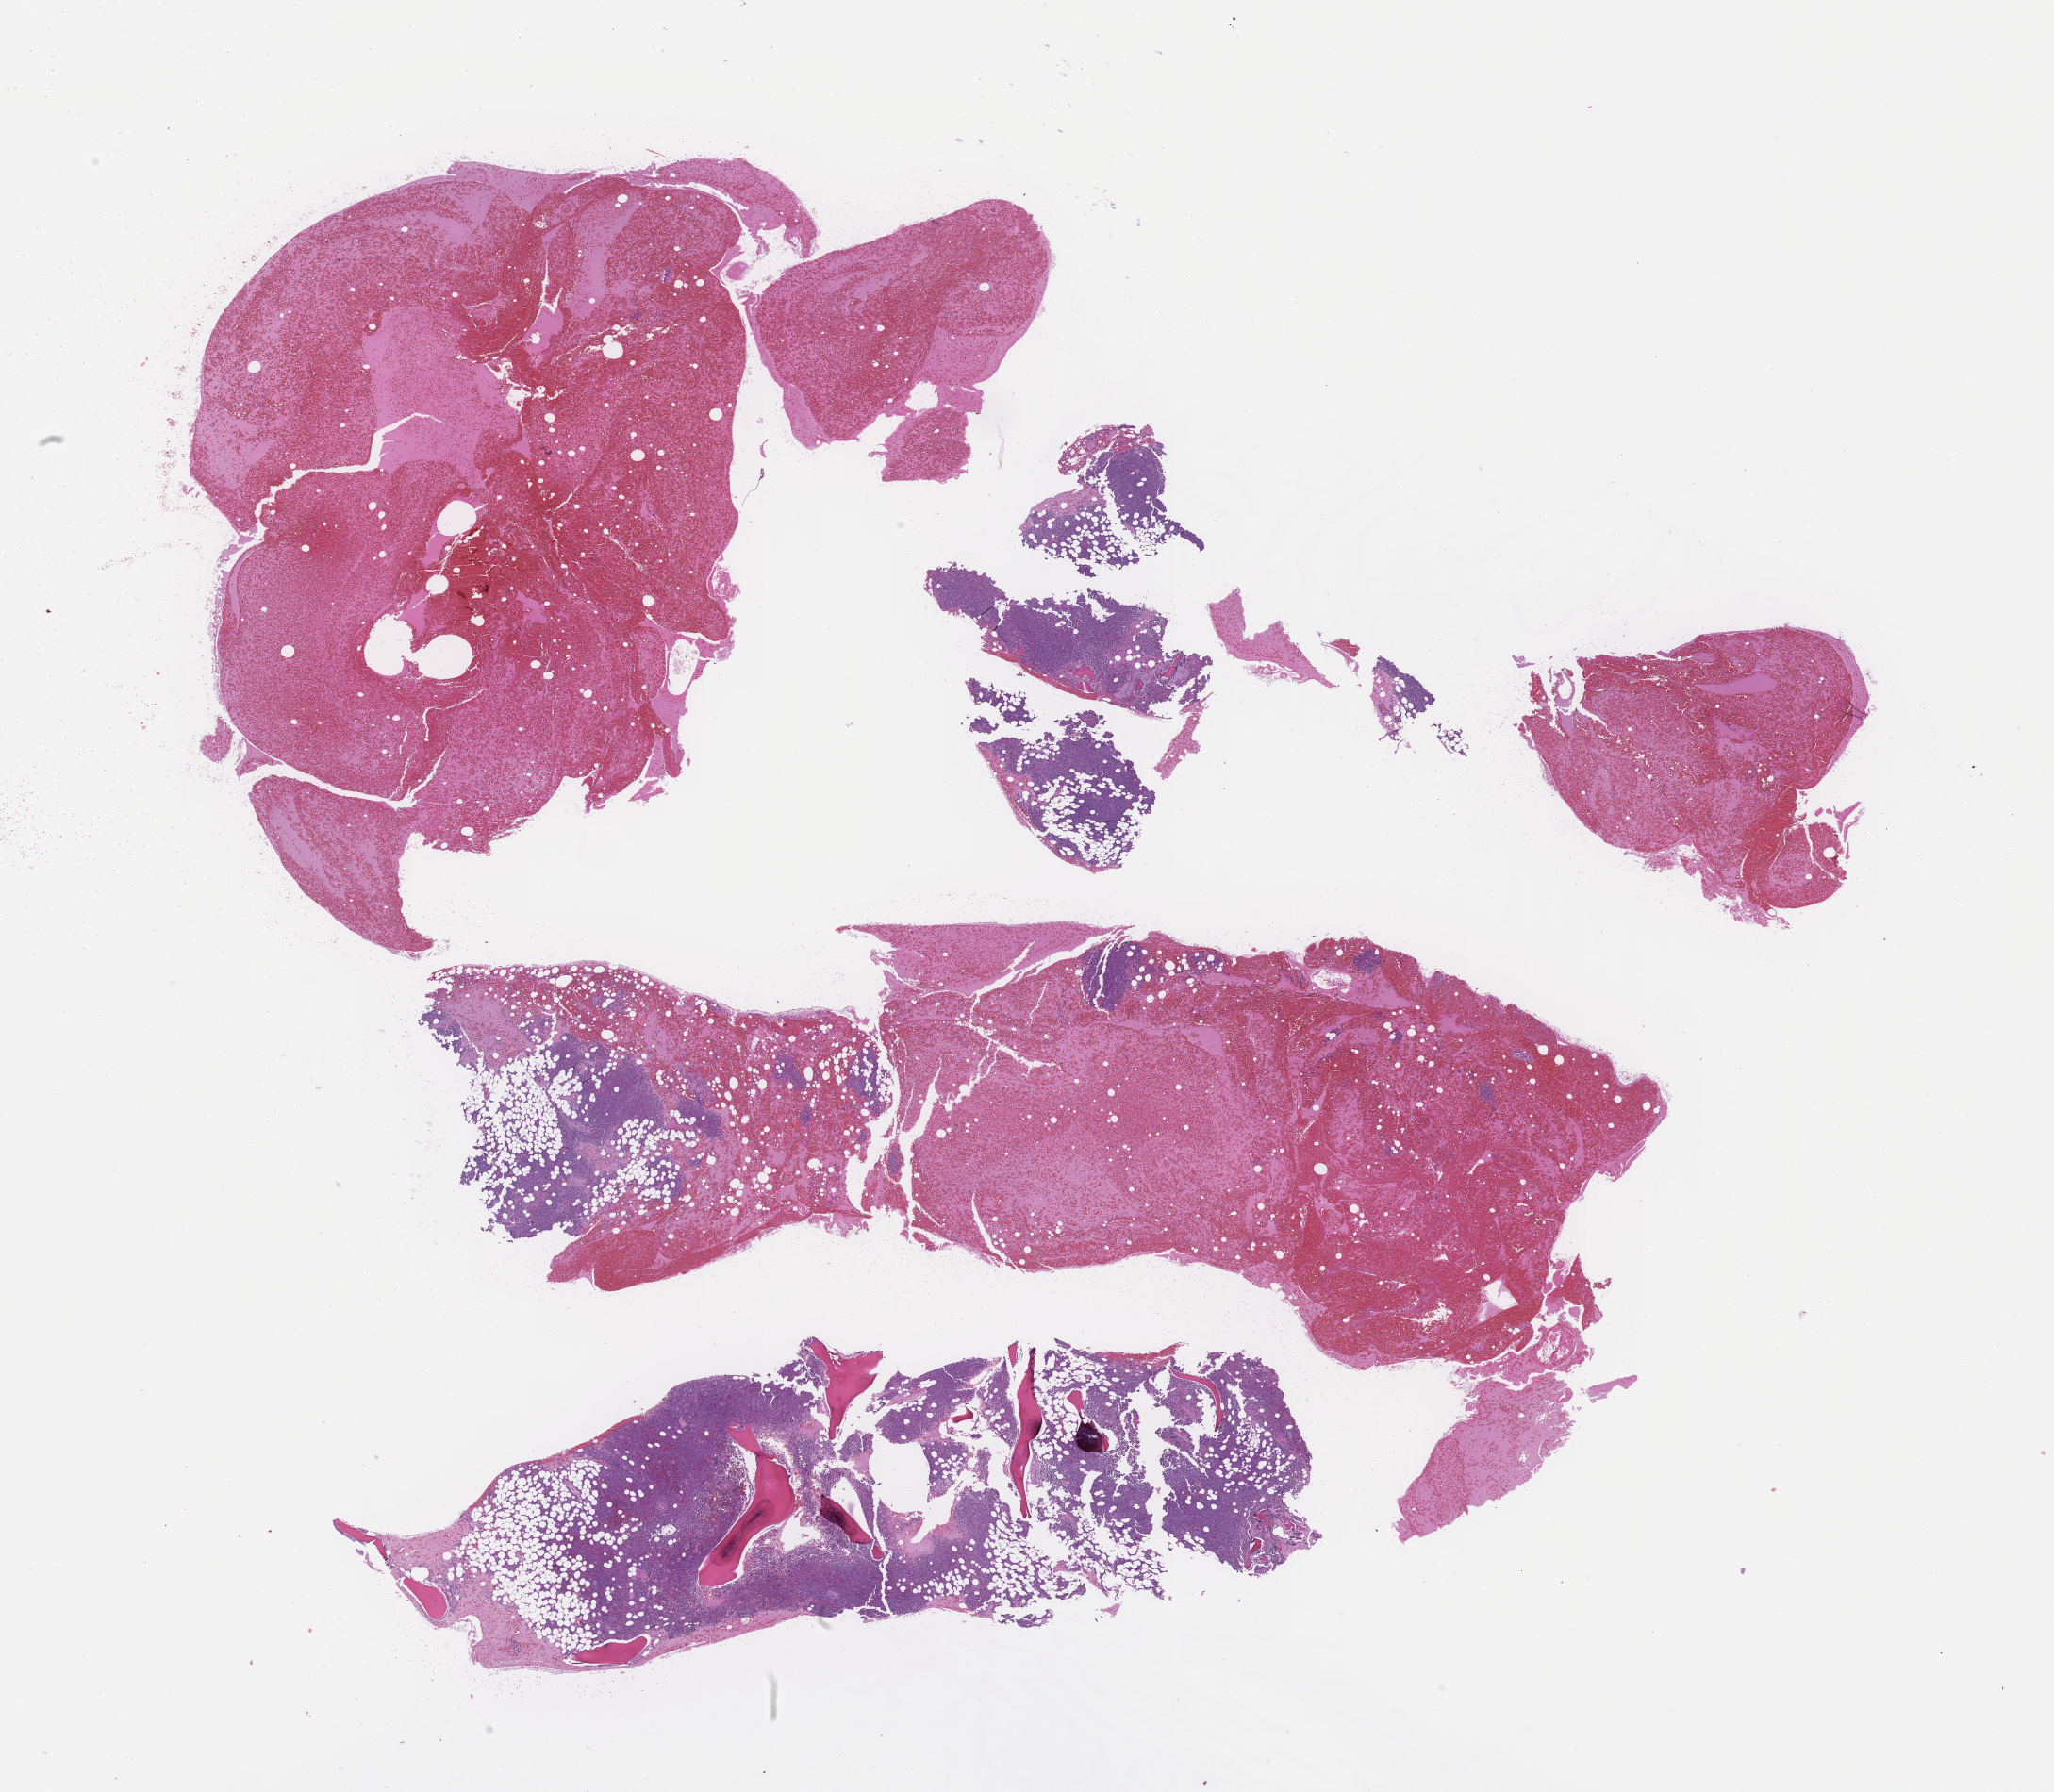
Whole-slide image, H&E stain — whole scanned area (about 17.6 x 15.3 mm) shown as a low-resolution overview; FFPE section; site: bone marrow; archival tissue. Patient sex: male.
This section: primary tumor. Diagnosis: Plasma Cell Myeloma.